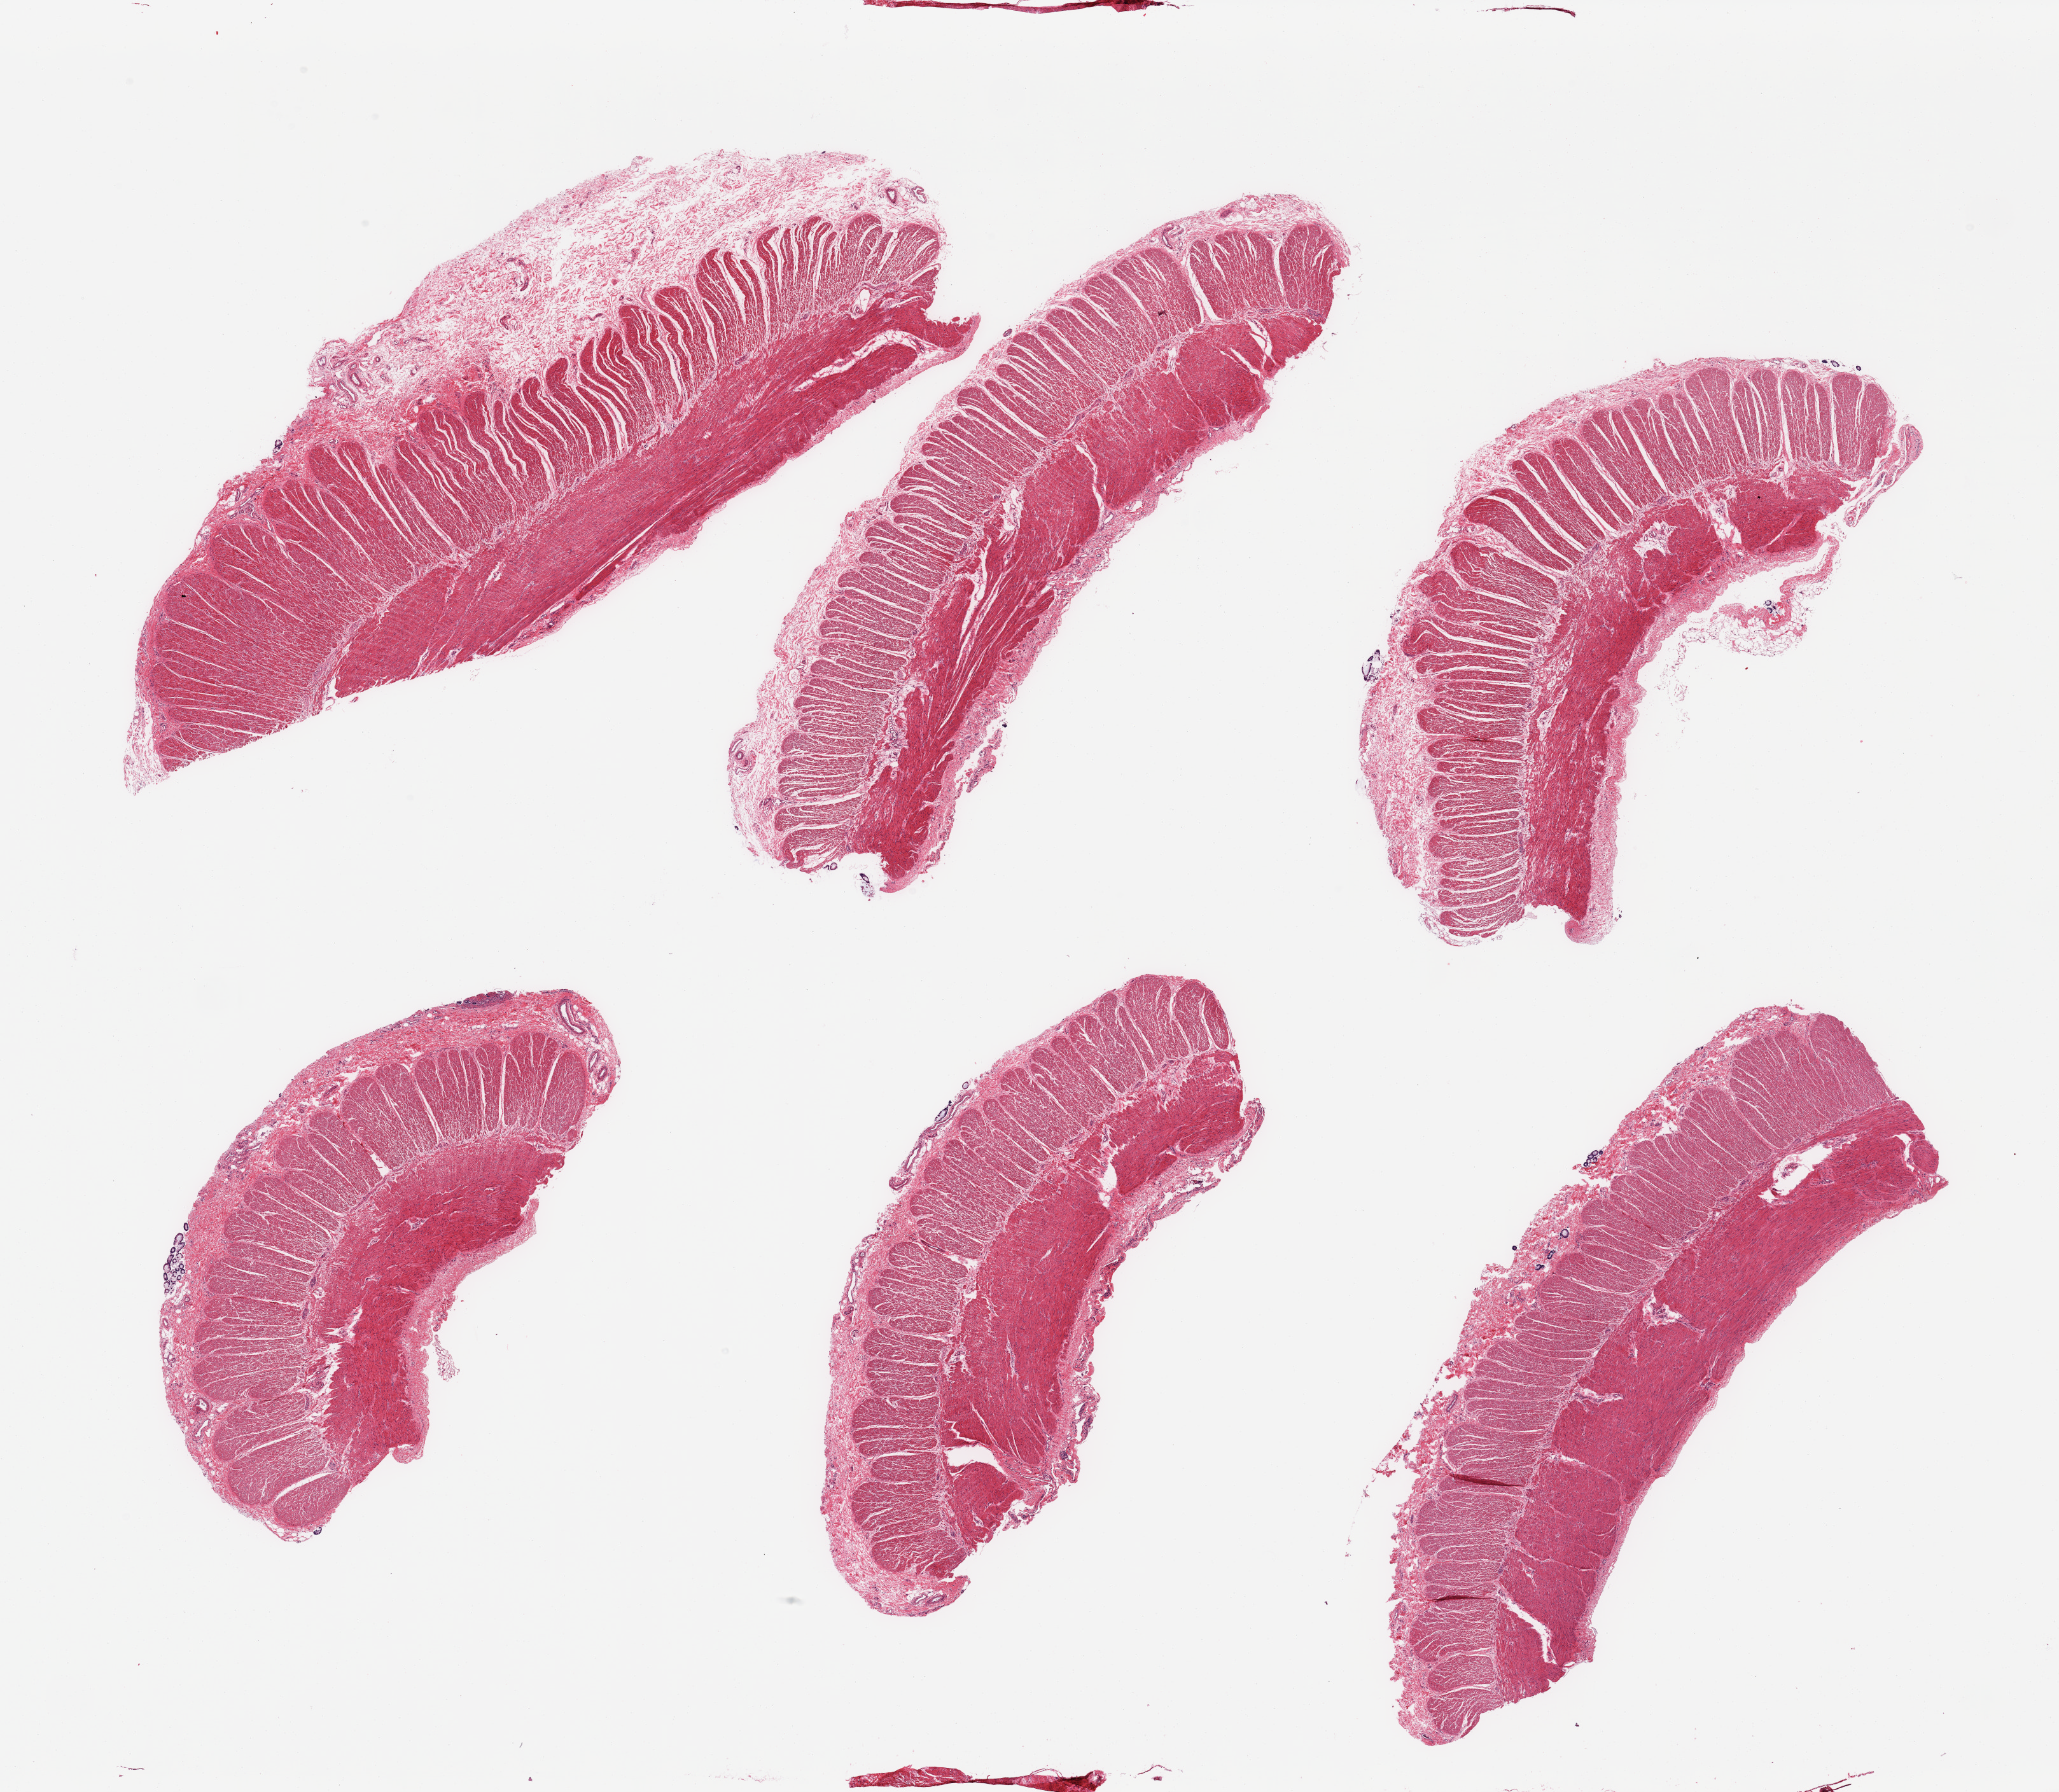
Haematoxylin and eosin whole-slide image, low-resolution overview of the scanned area, about 25.6 x 22.3 mm (acquisition: 20x scan), PAXgene-fixed, paraffin-embedded tissue, section of sigmoid colon (target tissue), tissue donor sample. Donor: female.
* review note (as recorded): 6 pieces; target muscularis and up to 1.5mm submucosa; scattered insignificant fragmented colonic glands